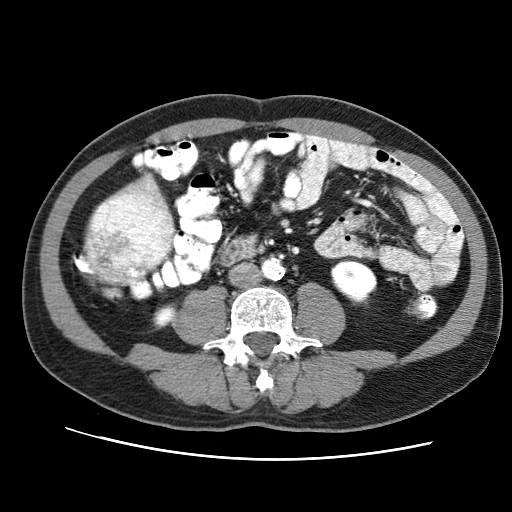
Contrast-enhanced abdominal CT (liver protocol), one axial slice; position 9 of 71 along the scan axis; soft-tissue window (W 400 / L 40 HU); 2.5 mm slice thickness; 512 × 512 image matrix, field of view 360 × 360 mm. Case-level facts recorded for this patient, not image findings: diagnosis: hepatocellular carcinoma (patient treated with transarterial chemoembolisation; whether this scan precedes or follows treatment is not stated here); TNM stage (as recorded): Stage-II; Child-Pugh class: A.
Outlined on this slice (semi-automatic segmentation, software-assisted and operator-edited):
- liver parenchyma outside the tumour (the mass and vessels are separate outlines, so this box may not span the whole liver): box from (x=84, y=173) to (x=178, y=284) px
- mass: (x=82, y=183)–(x=171, y=284)
- liver vessels: (x=143, y=180)–(x=173, y=273)